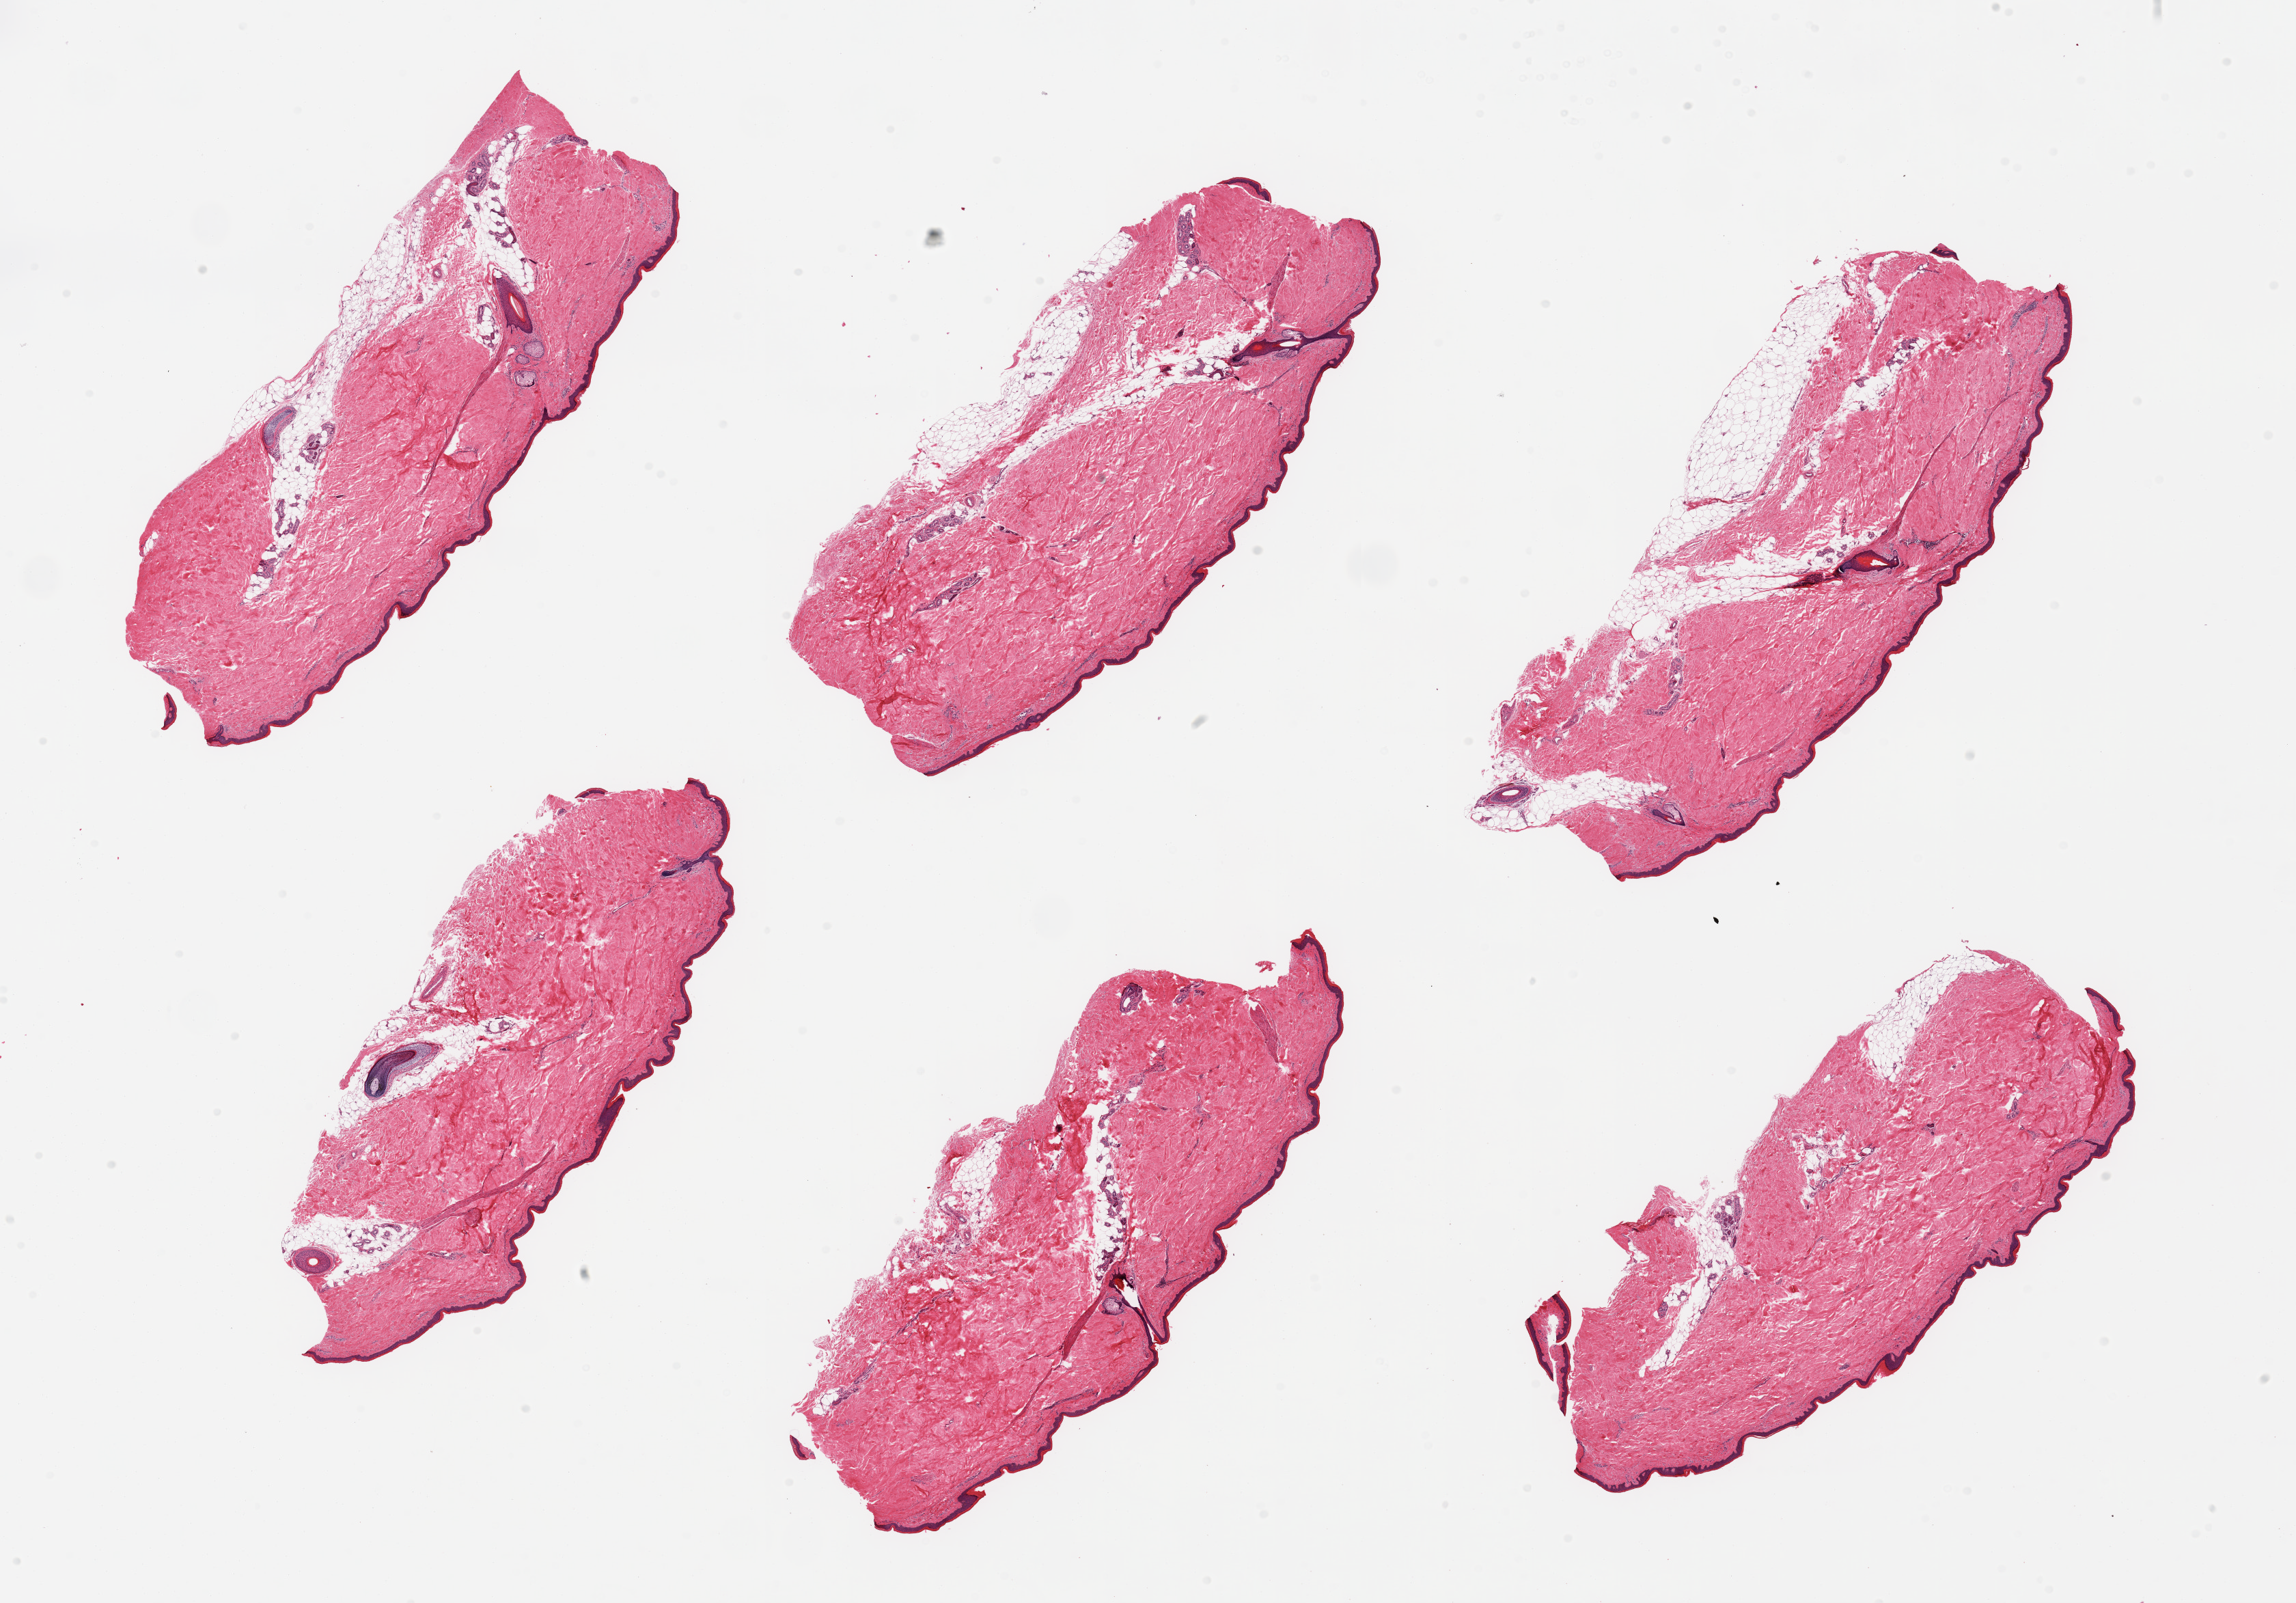
Whole-slide image, haematoxylin and eosin stain — low-resolution overview of the scanned area, about 26.6 x 18.6 mm (from a 20x scan). PAXgene-fixed paraffin-embedded (PFPE) section. Sampled site (target tissue): skin of lower leg. Tissue donor sample. Donor sex: male.
Pathologist's review note for this sample: 6 pieces; up to 20% dermal fat.